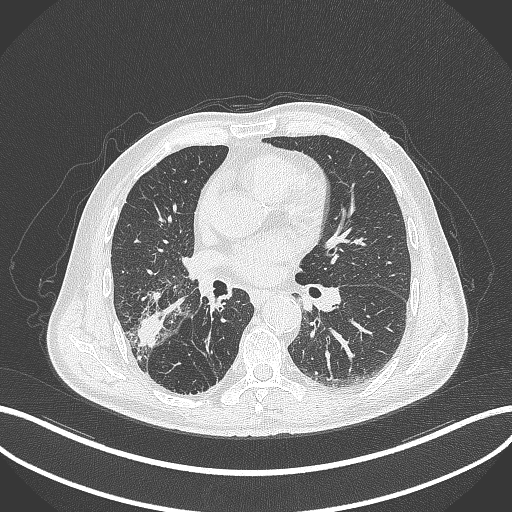
Chest CT, one axial slice. Slice 211 of 429 in the series (ordered by position). Reconstruction kernel B70f. 120 kVp. Lung window (W 1500 / L -600 HU). 512 × 512 image matrix. Patient: male, 72 years. Case-level facts recorded for this patient, not image findings: clinical TNM (as recorded): T3 N2 M0.
Outlined on this slice (rectangle marked by the reading radiologist):
- lung tumour (recorded histology: adenocarcinoma): box from (x=134, y=308) to (x=166, y=354) px